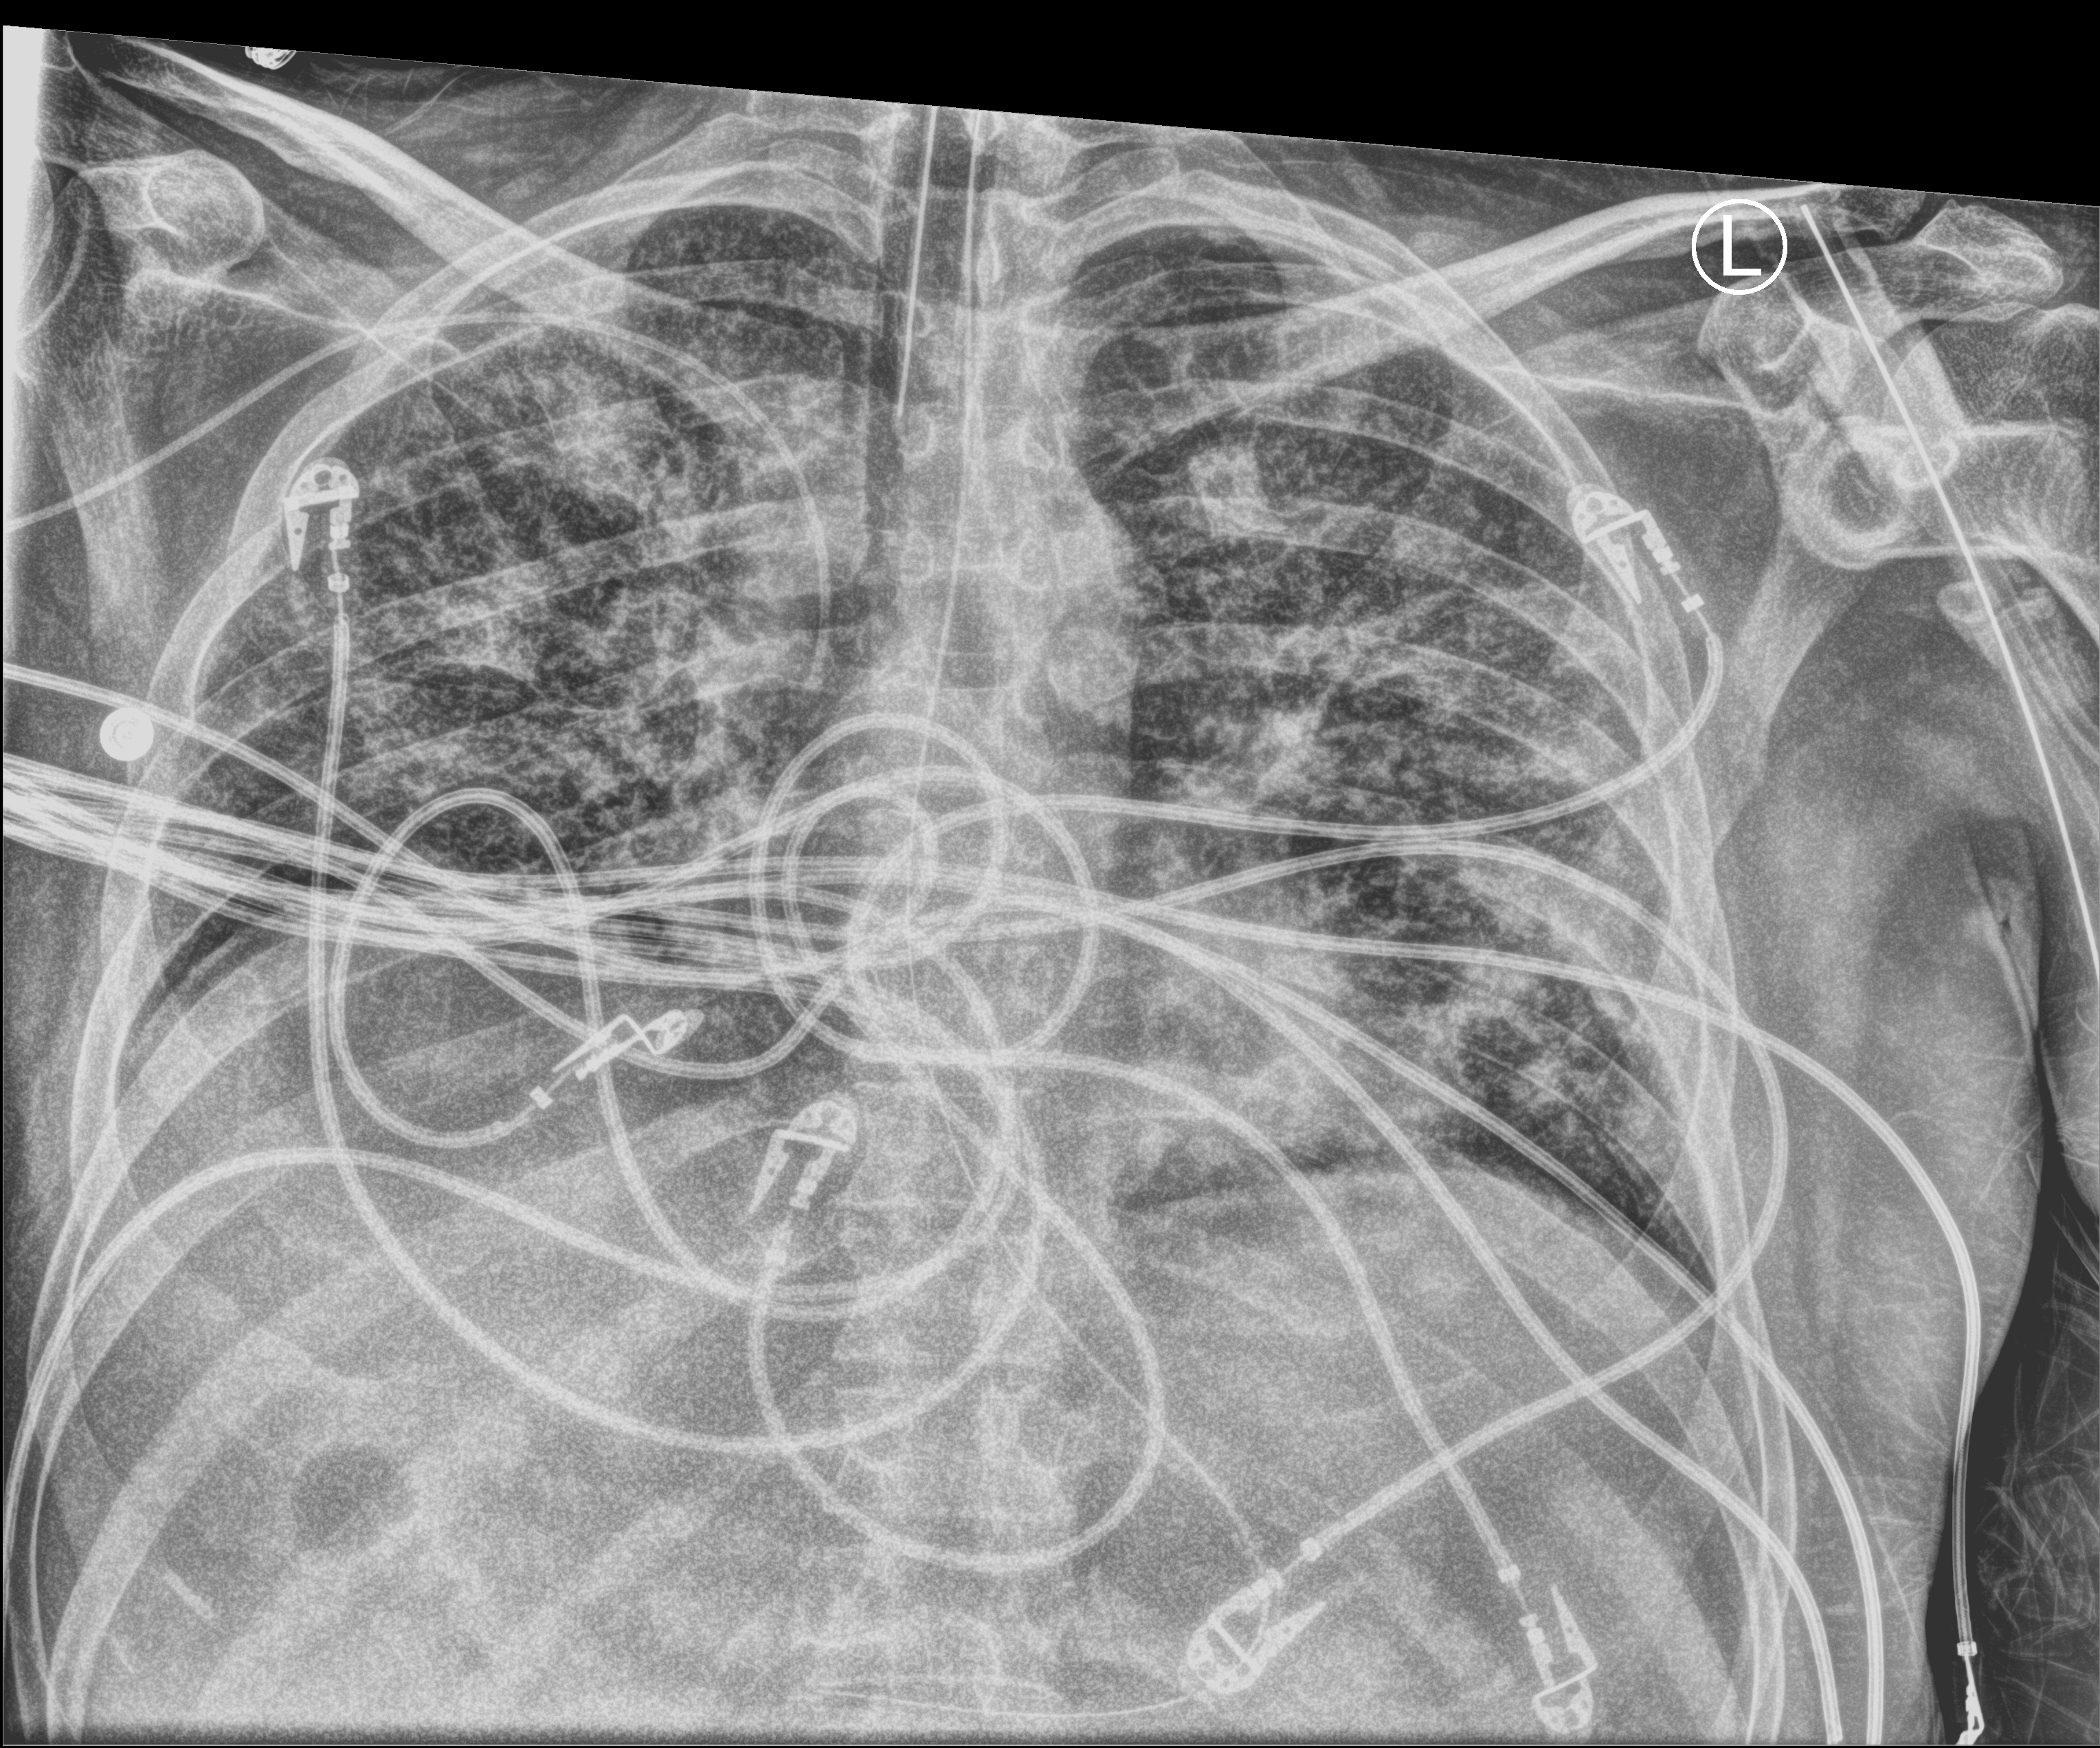
Chest X-ray (portable), anteroposterior (AP) projection. Male patient hospitalised with COVID-19, age 18–59 years.
From the hospital-stay record, not from the radiograph (when in the stay this image was taken is not recorded): diabetes (admission record): no; admitted to intensive care during this hospital stay: yes.